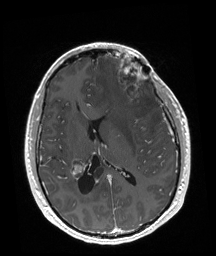
Brain MRI from a brain-tumour surgery series, one axial slice. Slice 85 of 192 in the series (ordered by position). T1-weighted post-contrast. 1 mm slice thickness. 216 × 256 image matrix, field of view 219 × 260 mm.
Outlined on this slice (expert manual segmentation):
- tumour: box from (x=116, y=57) to (x=146, y=102) px